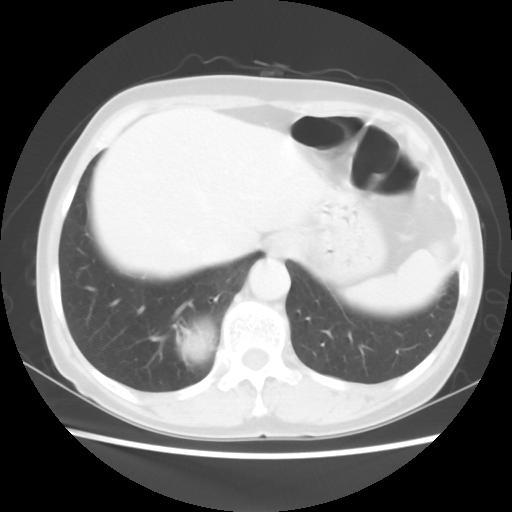
Chest CT, one axial slice; slice 9 of 56 in the series (ordered by position); 120 kVp; lung window (W 1500 / L -600 HU); 5 mm slice thickness; 512 × 512 image matrix, field of view 332 × 332 mm. Patient: female, 66 years. Case-level facts recorded for this patient, not image findings: clinical TNM (as recorded): T2 N3 M0; histopathological grade: G3.
Structures marked on this image (rectangle marked by the reading radiologist):
- lung tumour (recorded histology: small cell carcinoma): bounding box <183,324,216,363> (left, top, right, bottom; pixels)